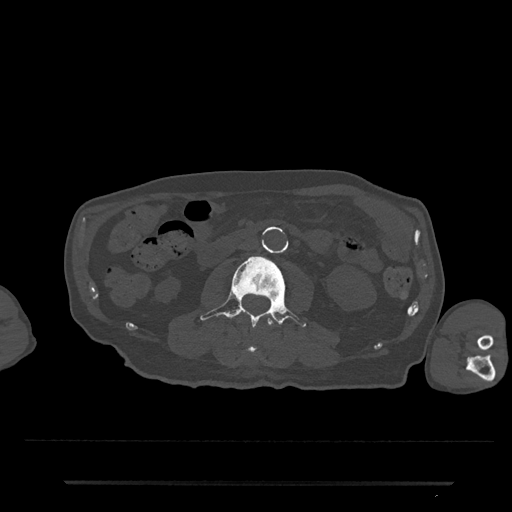
CT including the spine, one axial slice; position 3 of 797 along the scan axis; 120 kVp; bone window (W 1800 / L 400 HU); 512 × 512 image matrix, field of view 427 × 427 mm. Male patient, age 74 years. From the clinical record (not read from this slice): primary cancer: prostate.
Outlined on this slice (semi-automatic segmentation, software-assisted and operator-edited):
- L2 vertebra: bounding box [x1, y1, x2, y2] px = [245, 315, 276, 359]
- L3 vertebra: [199, 256, 306, 328]